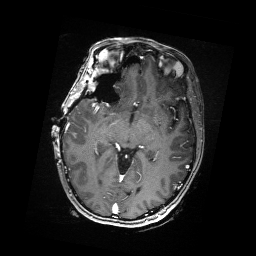
Brain MRI from a brain-tumour surgery series, one axial slice; position 100 of 176 along the scan axis; T1-weighted post-contrast; 256 × 256 image matrix. Case-level facts recorded for this patient, not image findings: histopathology: Metastatic Carcinoma from Breast primary; tumour location: Right Frontal.
Structures marked on this image (expert manual segmentation):
- residual tumour: bounding box (x1, y1, x2, y2) in pixels: (92, 69, 101, 86)